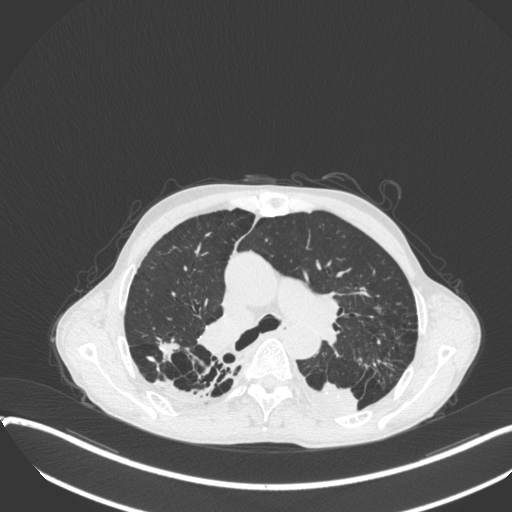
Chest CT, one axial slice. Slice 252 of 400 in the series (ordered by position). Lung window (W 1500 / L -600 HU). 1 mm slice thickness. 512 × 512 image matrix, field of view 400 × 400 mm. Male patient, age 57 years. Case-level facts recorded for this patient, not image findings: clinical TNM (as recorded): T4 N0 M0.
Outlined on this slice (rectangle marked by the reading radiologist):
- lung tumour (recorded histology: squamous cell carcinoma): bounding box (x1, y1, x2, y2) in pixels: (298, 376, 363, 420)